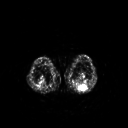
FDG PET of an extremity soft-tissue mass (from a PET/CT study), one axial slice; slice 175 of 267 in the series (ordered by position); 3.27 mm slice thickness; 128 × 128 image matrix. Patient: male, 54 years. Case-level facts recorded for this patient, not image findings: histological type: synovial sarcoma; site of the primary tumour: left poplietal fossa.
Outlined on this slice (expert contour drawn on MRI and transferred to this co-registered scan by the dataset authors):
- gross tumour volume (mass): box from (x=82, y=85) to (x=87, y=90) px